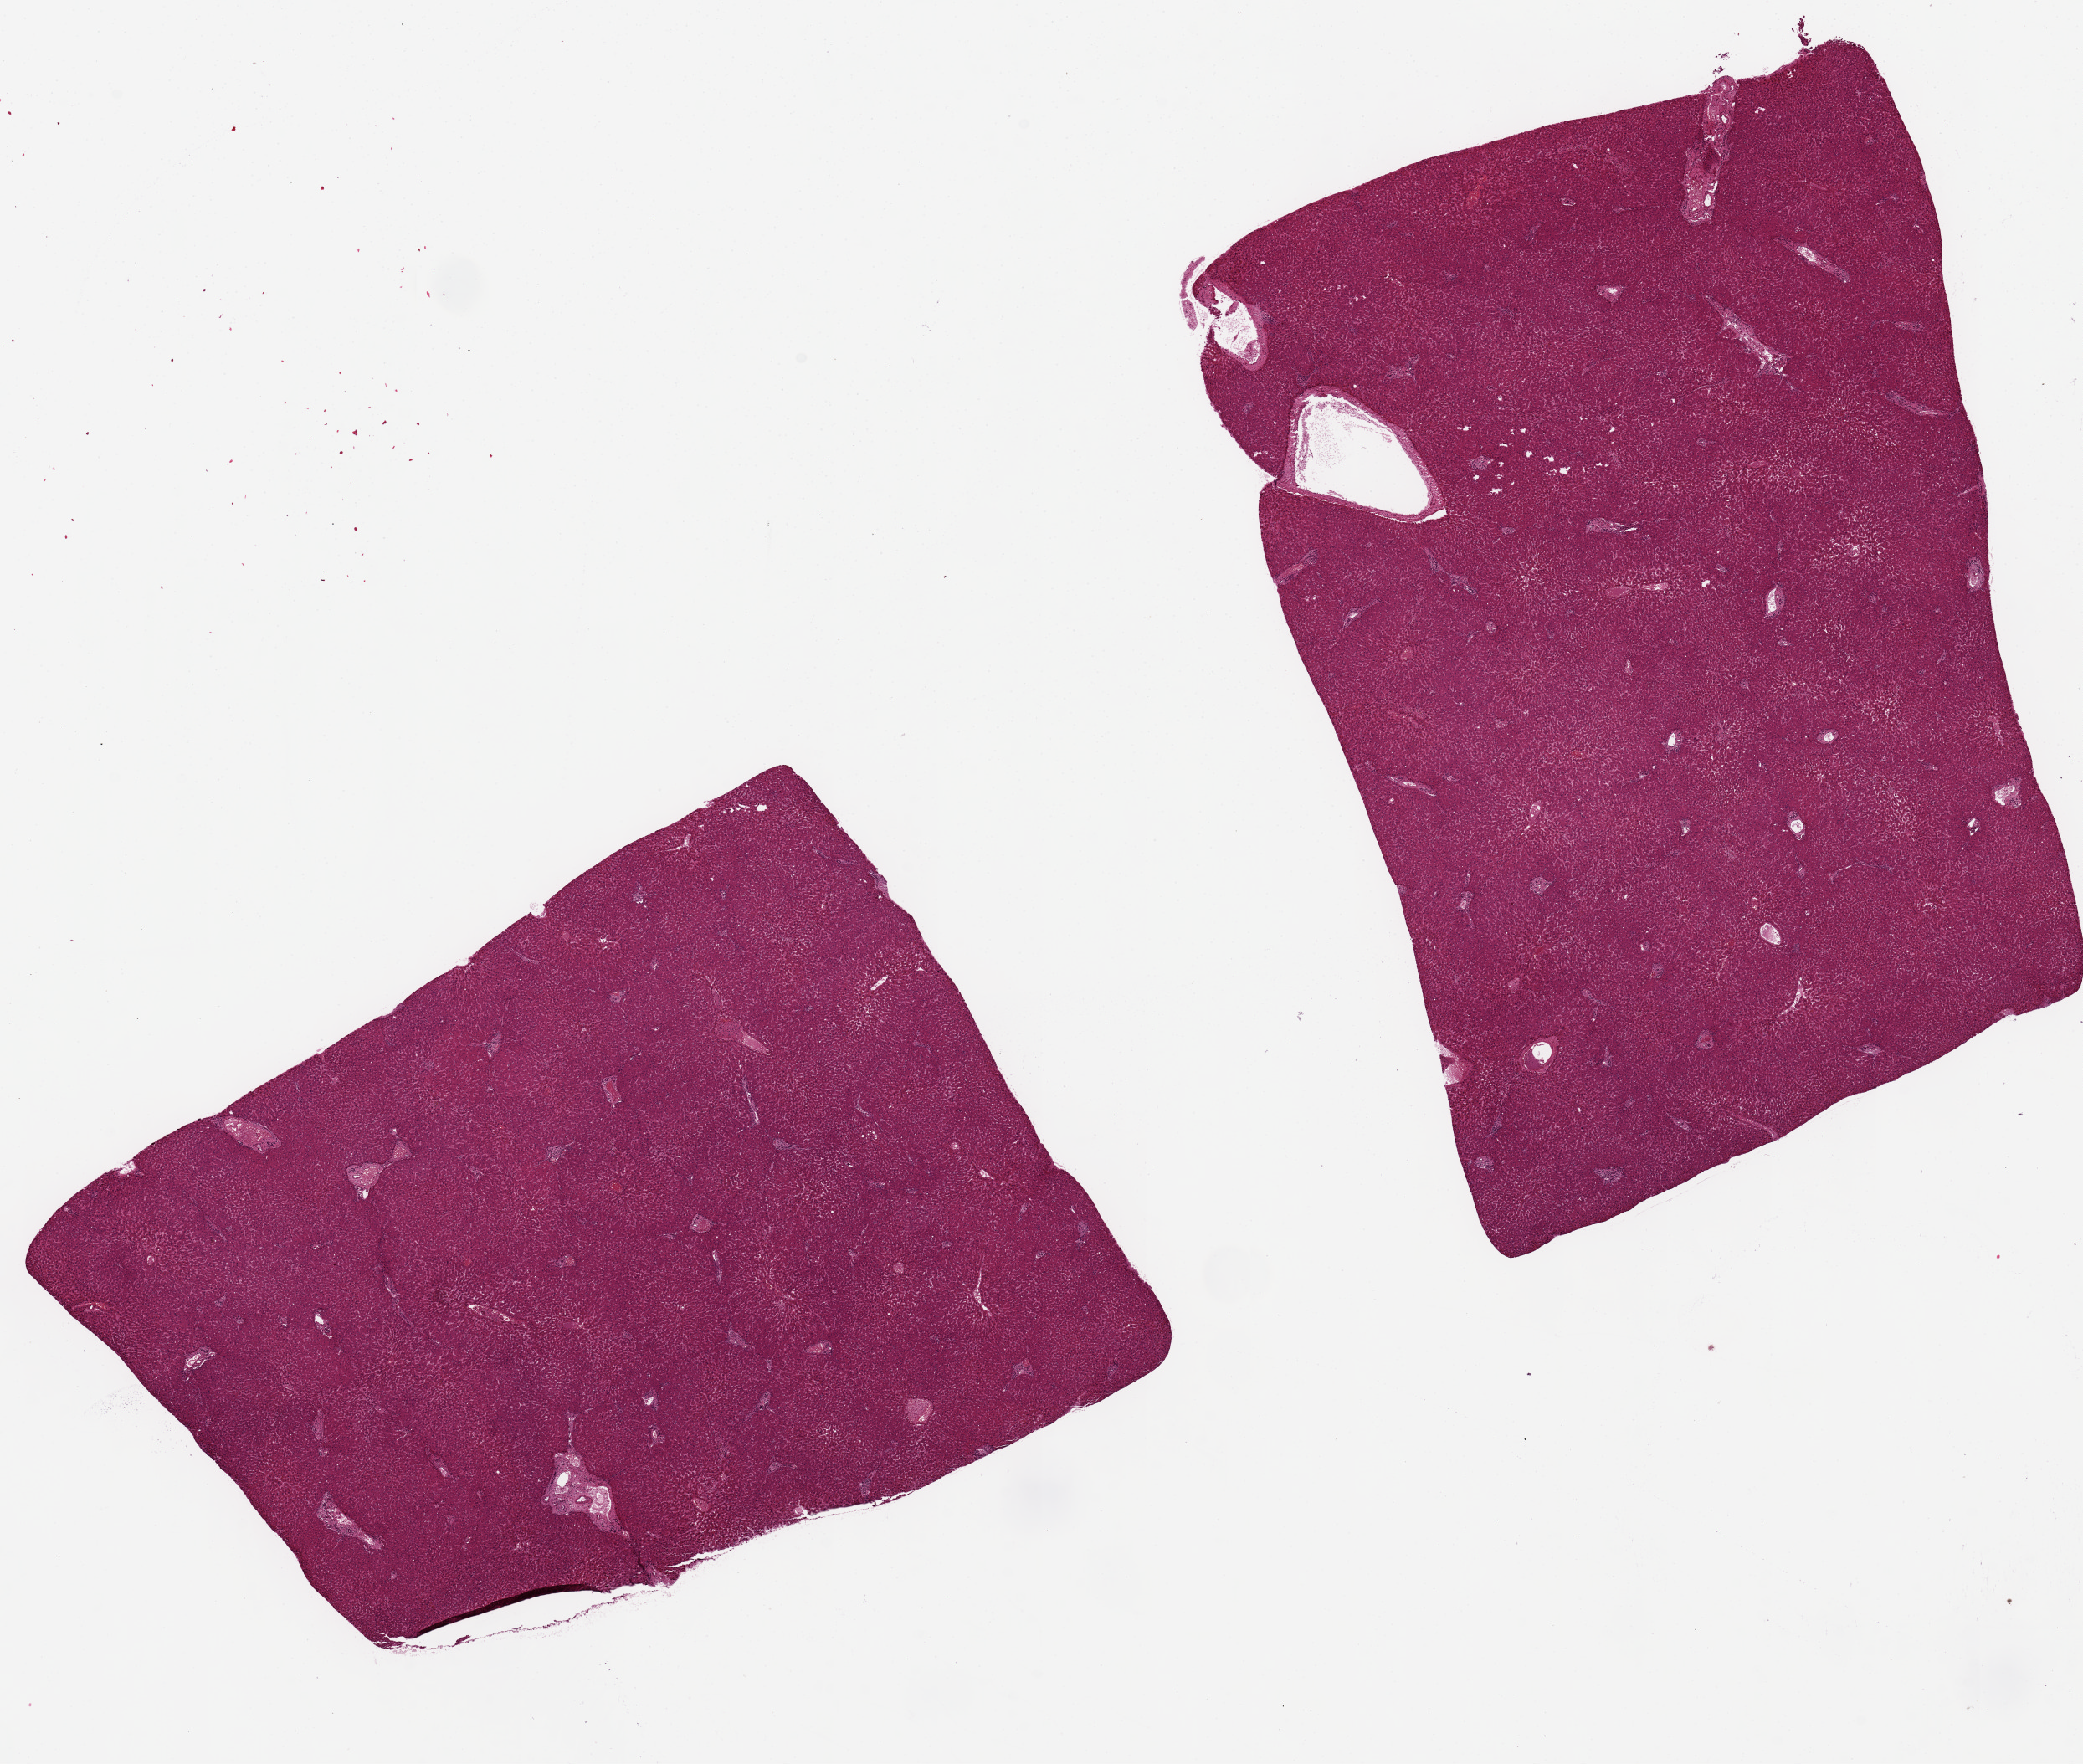
Hematoxylin and eosin (H&E) whole-slide image, brightfield — shown as a low-resolution overview of the whole scanned area (about 19.7 x 16.7 mm); PAXgene-fixed, paraffin-embedded tissue; sampled site (target tissue): liver; tissue donor sample. Donor: male.
- reviewer comment on this tissue sample: 2 pieces 10x7&8x6.7 mm; good preservation, no lesions